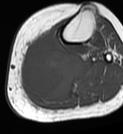
MRI of an extremity soft-tissue mass, one axial slice; position 35 of 68 along the scan axis; MR volume resampled by the dataset authors to the PET/CT grid (not the native acquisition matrix); 123 × 134 image matrix, field of view 120 × 131 mm. Female patient. Case-level facts recorded for this patient, not image findings: histological type: extraskeletal high grade osteogenic sarcoma; grade: high; site of the primary tumour: left calf.
Structures marked on this image (expert contour drawn on MRI and transferred to this co-registered scan by the dataset authors):
- gross tumour volume (mass): bounding box <22,32,84,99> (left, top, right, bottom; pixels)